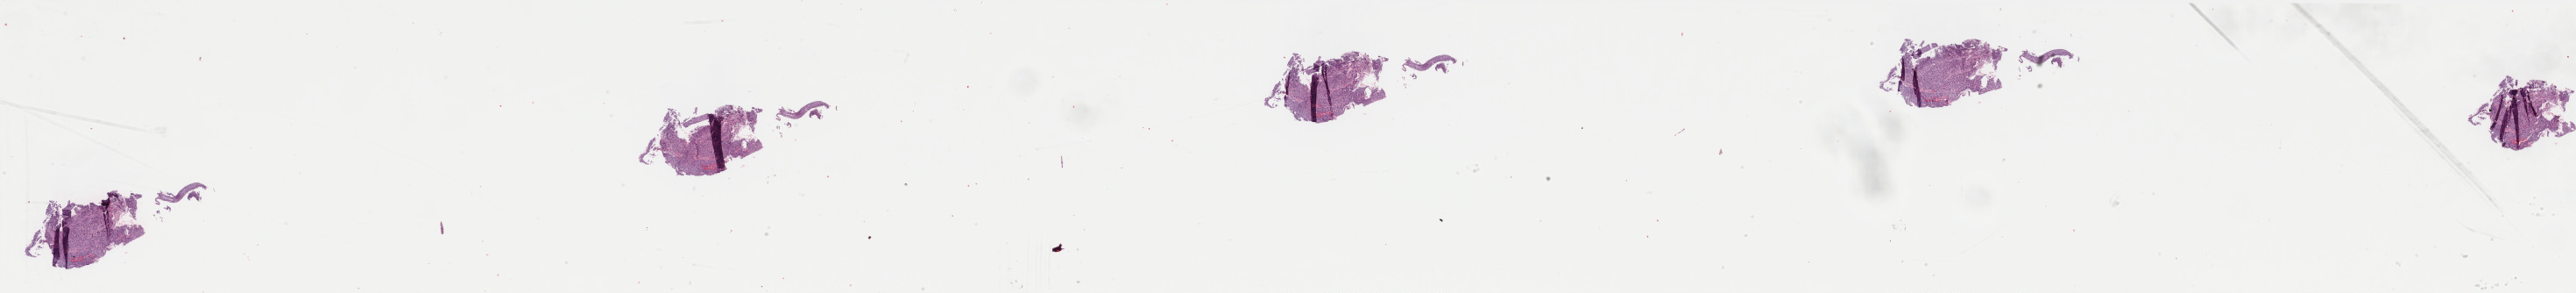
H&E whole-slide image — shown as a low-resolution overview of the whole scanned area (about 47.1 x 5.3 mm, acquisition: 40x scan), formalin-fixed paraffin-embedded (FFPE) diagnostic section, sample: primary tumour, cervix. Patient: female, age at initial diagnosis 50 years. Histologic grade: G2 (moderately differentiated).
Diagnosis: Squamous cell carcinoma, NOS (cervix uteri). FIGO stage: IB1.